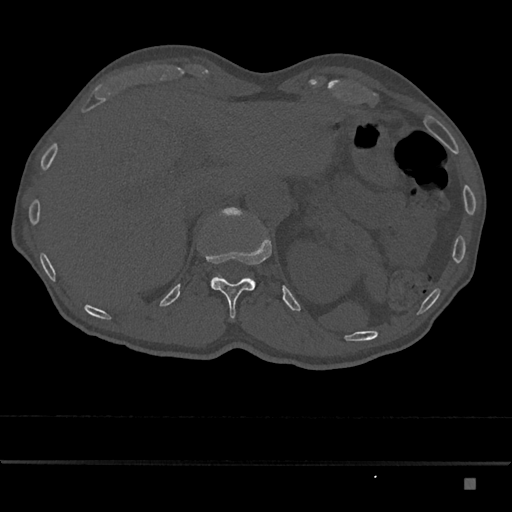
CT including the spine, one axial slice. Position 599 of 797 along the scan axis. Reconstruction kernel Br40s/3. Bone window (W 1800 / L 400 HU). 0.5 mm slice thickness. 512 × 512 image matrix, field of view 390 × 390 mm. Patient: male, 72 years. From the clinical record (not read from this slice): primary cancer: prostate.
Structures marked on this image (semi-automatically segmented with operator editing):
- L1 vertebra: box from (x=211, y=207) to (x=243, y=282) px
- T12 vertebra: (x=206, y=237)–(x=272, y=319)